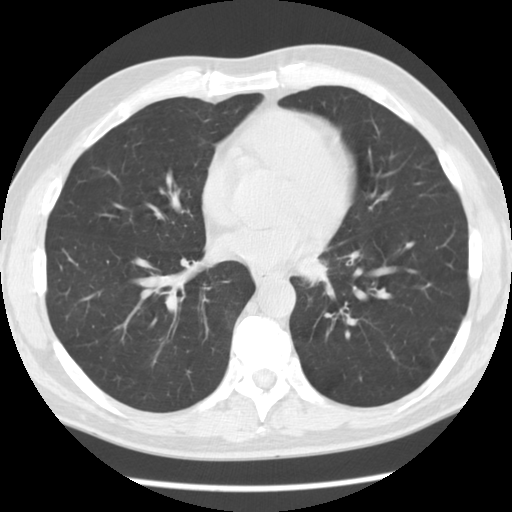
Chest CT (low-dose screening protocol), one axial image; baseline screening round; lung window (W 1500 / L -600 HU); 2.5 mm slice thickness; slice 67 of 112 in the series; 512 × 512 image matrix, field of view 340 × 340 mm. Male, age 55 years at enrolment. Former smoker at enrolment.
Expert-annotated lung lesion, box from (x=284, y=235) to (x=345, y=294) px. No non-calcified nodule or mass ≥4 mm was recorded by the screening reader at this exam. Official screen result: negative screen, minor abnormalities not suspicious for lung cancer. Later outcome: lung cancer diagnosed 223 days after this screen — squamous cell carcinoma, NOS, left lower lobe, moderately differentiated (G2), stage IV (AJCC 6th edition), 51 mm at pathology.